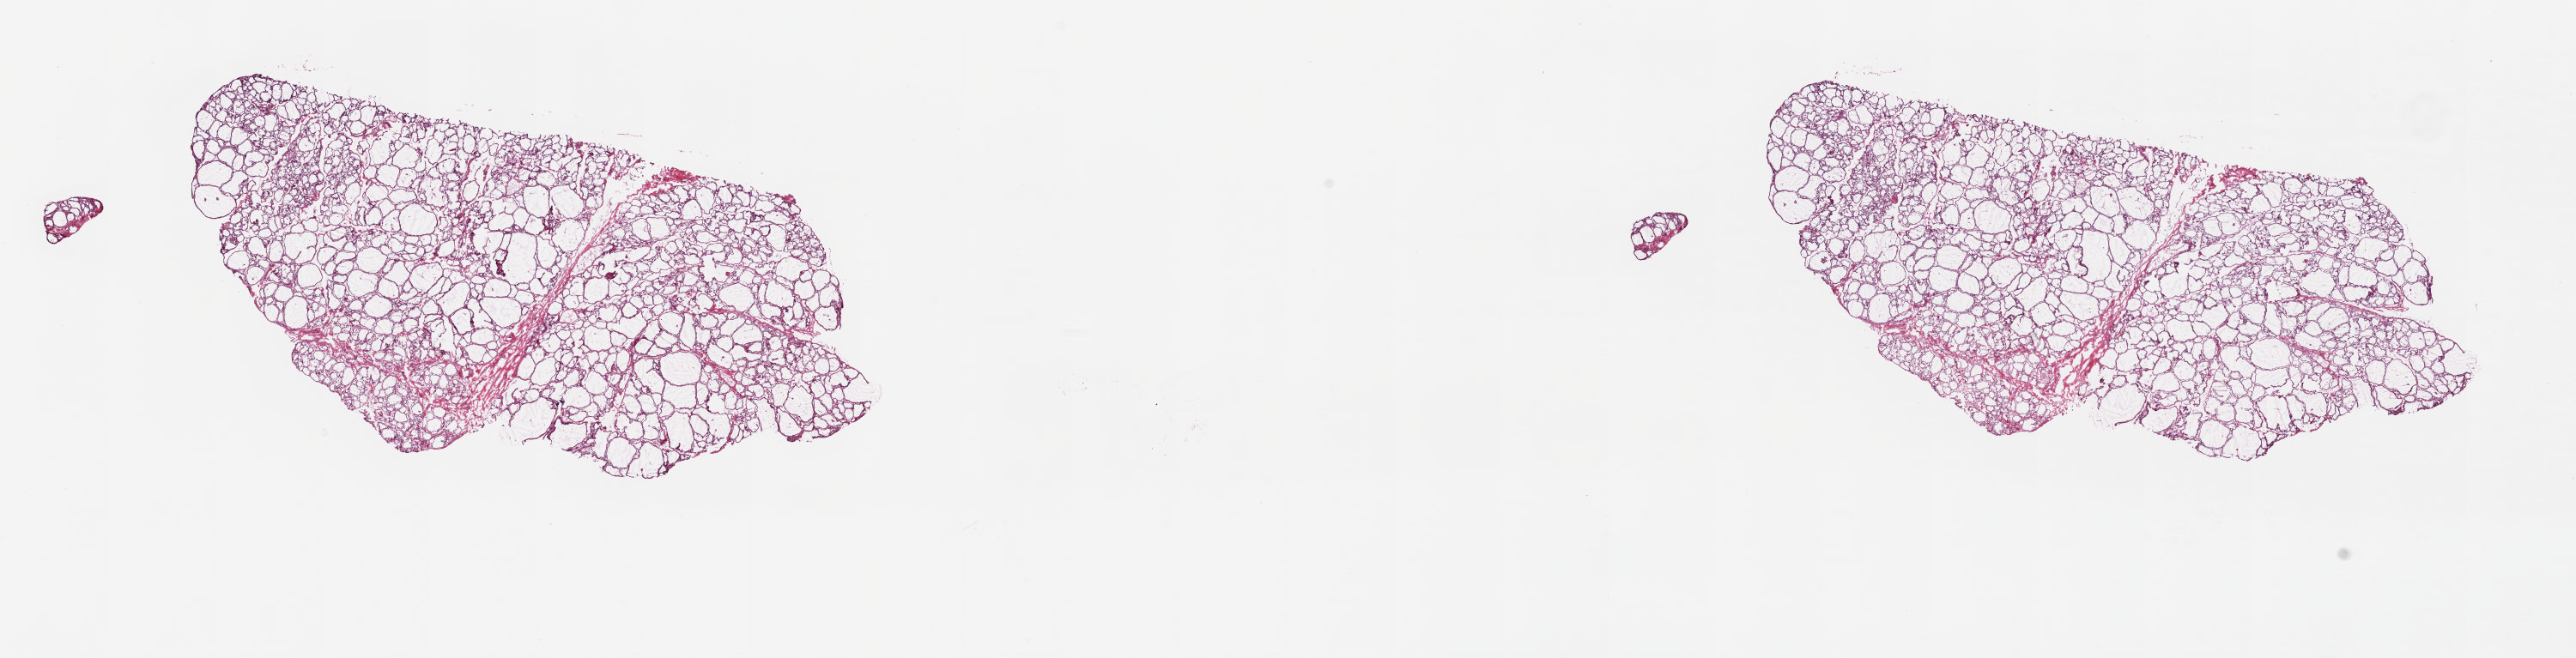
H&E whole-slide image — a low-resolution overview of the entire scanned area, about 23.8 x 6.1 mm (acquisition: 20x scan), frozen section from the top of the tissue portion, sample: solid tissue normal (non-tumour tissue), thyroid. Female patient; age at initial diagnosis 39 years. Composition of this section per pathologist review: tumour cells 0%, tumour nuclei 0%, normal cells 100%, stromal cells 0%, necrosis 0%. Inflammatory infiltration, as recorded: lymphocyte infiltration 0%, monocyte infiltration 0%, neutrophil infiltration 0%.
• this section: solid tissue normal sample (biorepository sample class)
• patient diagnosis: Papillary carcinoma, follicular variant (thyroid gland)